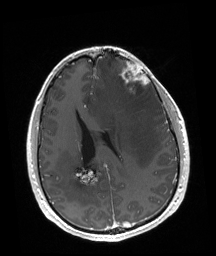
Brain MRI from a brain-tumour surgery series, one axial slice; slice 72 of 192 in the series (ordered by position); T1-weighted post-contrast; 1 mm slice thickness; 216 × 256 image matrix, field of view 219 × 260 mm.
Structures marked on this image (expert manual segmentation):
- tumour: bounding box [x1, y1, x2, y2] px = [121, 63, 149, 93]